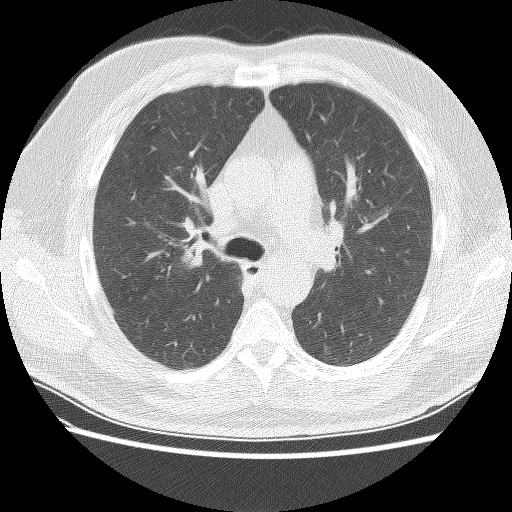
Low-dose screening chest CT, axial slice; first (baseline) screen; lung window (W 1500 / L -600 HU); 2.5 mm slice thickness; 120 kVp; slice 64 of 159 in the series; 512 × 512 image matrix, field of view 360 × 360 mm. Male, age 57 years at enrolment. Current smoker at enrolment.
- Lesion marked by an expert reader, box from (x=160, y=238) to (x=214, y=294) px.
- No non-calcified nodule or mass ≥4 mm was recorded by the screening reader at this exam.
- Participant outcome: lung cancer diagnosed 434 days after this screen (after the second annual screen) — non-small cell carcinoma, right upper lobe, poorly differentiated (G3), stage IIA (AJCC 6th edition), 25 mm at pathology.